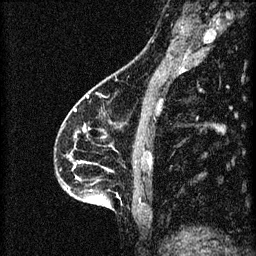
Breast MRI (dynamic contrast-enhanced), one sagittal slice; 3 images stored at this slice position (order not interpretable as contrast timing); 1.5 T; TE 4.2 ms, TR 8.2 ms; 2 mm slice thickness; 256 × 256 image matrix. Patient: female, 46 years.
Annotated regions visible in this slice (semi-automatically segmented with operator editing):
- analysis volume of interest (the breast-tissue region the enhancement analysis was run in; not a lesion): box from (x=55, y=114) to (x=148, y=209) px
- tumour enhancement mask (voxels above the 70 % enhancement threshold inside the analysis volume of interest): (x=83, y=128)–(x=90, y=133)